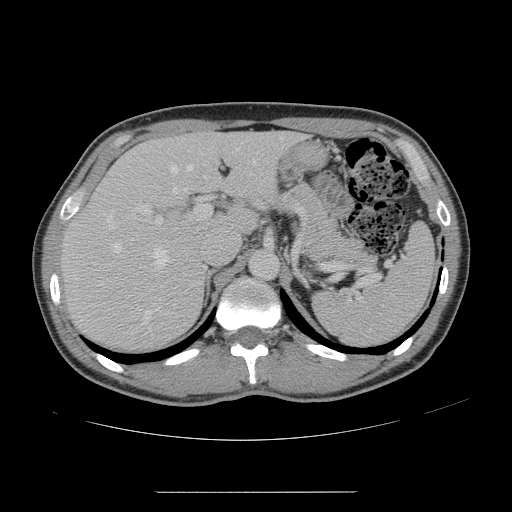
Contrast-enhanced abdominal CT, one axial slice; slice 100 of 178 in the series (ordered by position); intravenous contrast given; soft-tissue window (W 400 / L 40 HU); 2.5 mm slice thickness; 512 × 512 image matrix, field of view 401 × 401 mm. Male patient, age 53 years. From the clinical record (not read from this slice): diagnosis: colorectal cancer liver metastases, imaged before liver resection; multiple liver metastases: yes; largest metastasis: 2.4 cm; chemotherapy before resection: yes.
Structures marked on this image (manually delineated by an expert):
- hepatic veins: box from (x=111, y=147) to (x=238, y=322) px
- liver: (x=63, y=134)–(x=300, y=349)
- planned liver remnant (the part of the liver to remain after resection): (x=147, y=134)–(x=299, y=229)
- portal vein (with intrahepatic branches): (x=133, y=204)–(x=212, y=227)